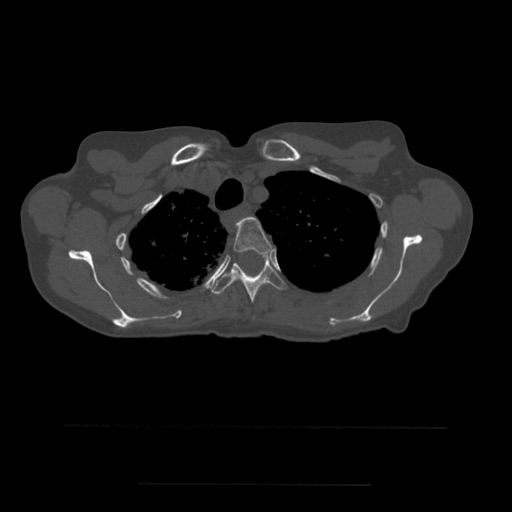
CT including the spine, one axial slice; slice 414 of 544 in the series (ordered by position); bone window (W 1800 / L 400 HU); 512 × 512 image matrix. Patient age 58 years. Case-level facts recorded for this patient, not image findings: primary cancer: lung.
Annotated regions visible in this slice (semi-automatic segmentation, software-assisted and operator-edited):
- T2 vertebra: bounding box <236,222,242,225> (left, top, right, bottom; pixels)
- T3 vertebra: <234,217,274,255>
- T4 vertebra: <212,253,289,303>